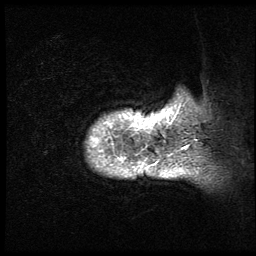
Breast MRI (dynamic contrast-enhanced), one sagittal slice; slice 5 of 64 in the series (ordered by position); 3 images stored at this slice position (order not interpretable as contrast timing); 1.5 T; TE 4.2 ms, TR 9 ms; 2.5 mm slice thickness; 256 × 256 image matrix. Patient: female, 50 years. Case-level facts recorded for this patient, not image findings: setting: breast cancer imaged before/during neoadjuvant chemotherapy; receptor status: triple-negative.
Annotated regions visible in this slice (semi-automatic segmentation, software-assisted and operator-edited):
- analysis volume of interest (the breast-tissue region the enhancement analysis was run in; not a lesion): bounding box (x1, y1, x2, y2) in pixels: (80, 79, 194, 211)
- tumour enhancement mask (voxels above the 140 % enhancement threshold inside the analysis volume of interest): (86, 109, 189, 178)